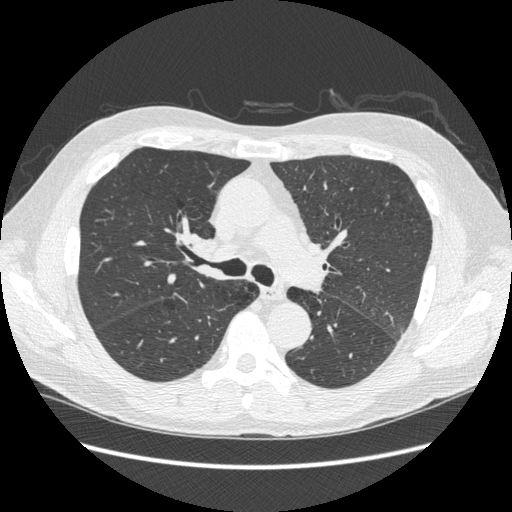
Low-dose screening chest CT, axial slice. Third screening round (two years after baseline). Lung window (W 1500 / L -600 HU). 1.25 mm slice thickness. Standard (soft-tissue) reconstruction kernel (STANDARD). 120 kVp. Slice 103 of 258 in the series. Male, age 59 years at enrolment. Current smoker at enrolment.
Expert reader's lesion annotation, bounding box [x1, y1, x2, y2] px = [177, 225, 227, 270]. The screening reader recorded 2 non-calcified nodules or masses ≥4 mm on this exam; which of them this box marks is not recorded. Official screen result: negative screen, minor abnormalities not suspicious for lung cancer. Later outcome: lung cancer diagnosed 169 days after this screen — squamous cell carcinoma, keratinizing, NOS, right hilum, stage IIIB (AJCC 6th edition).